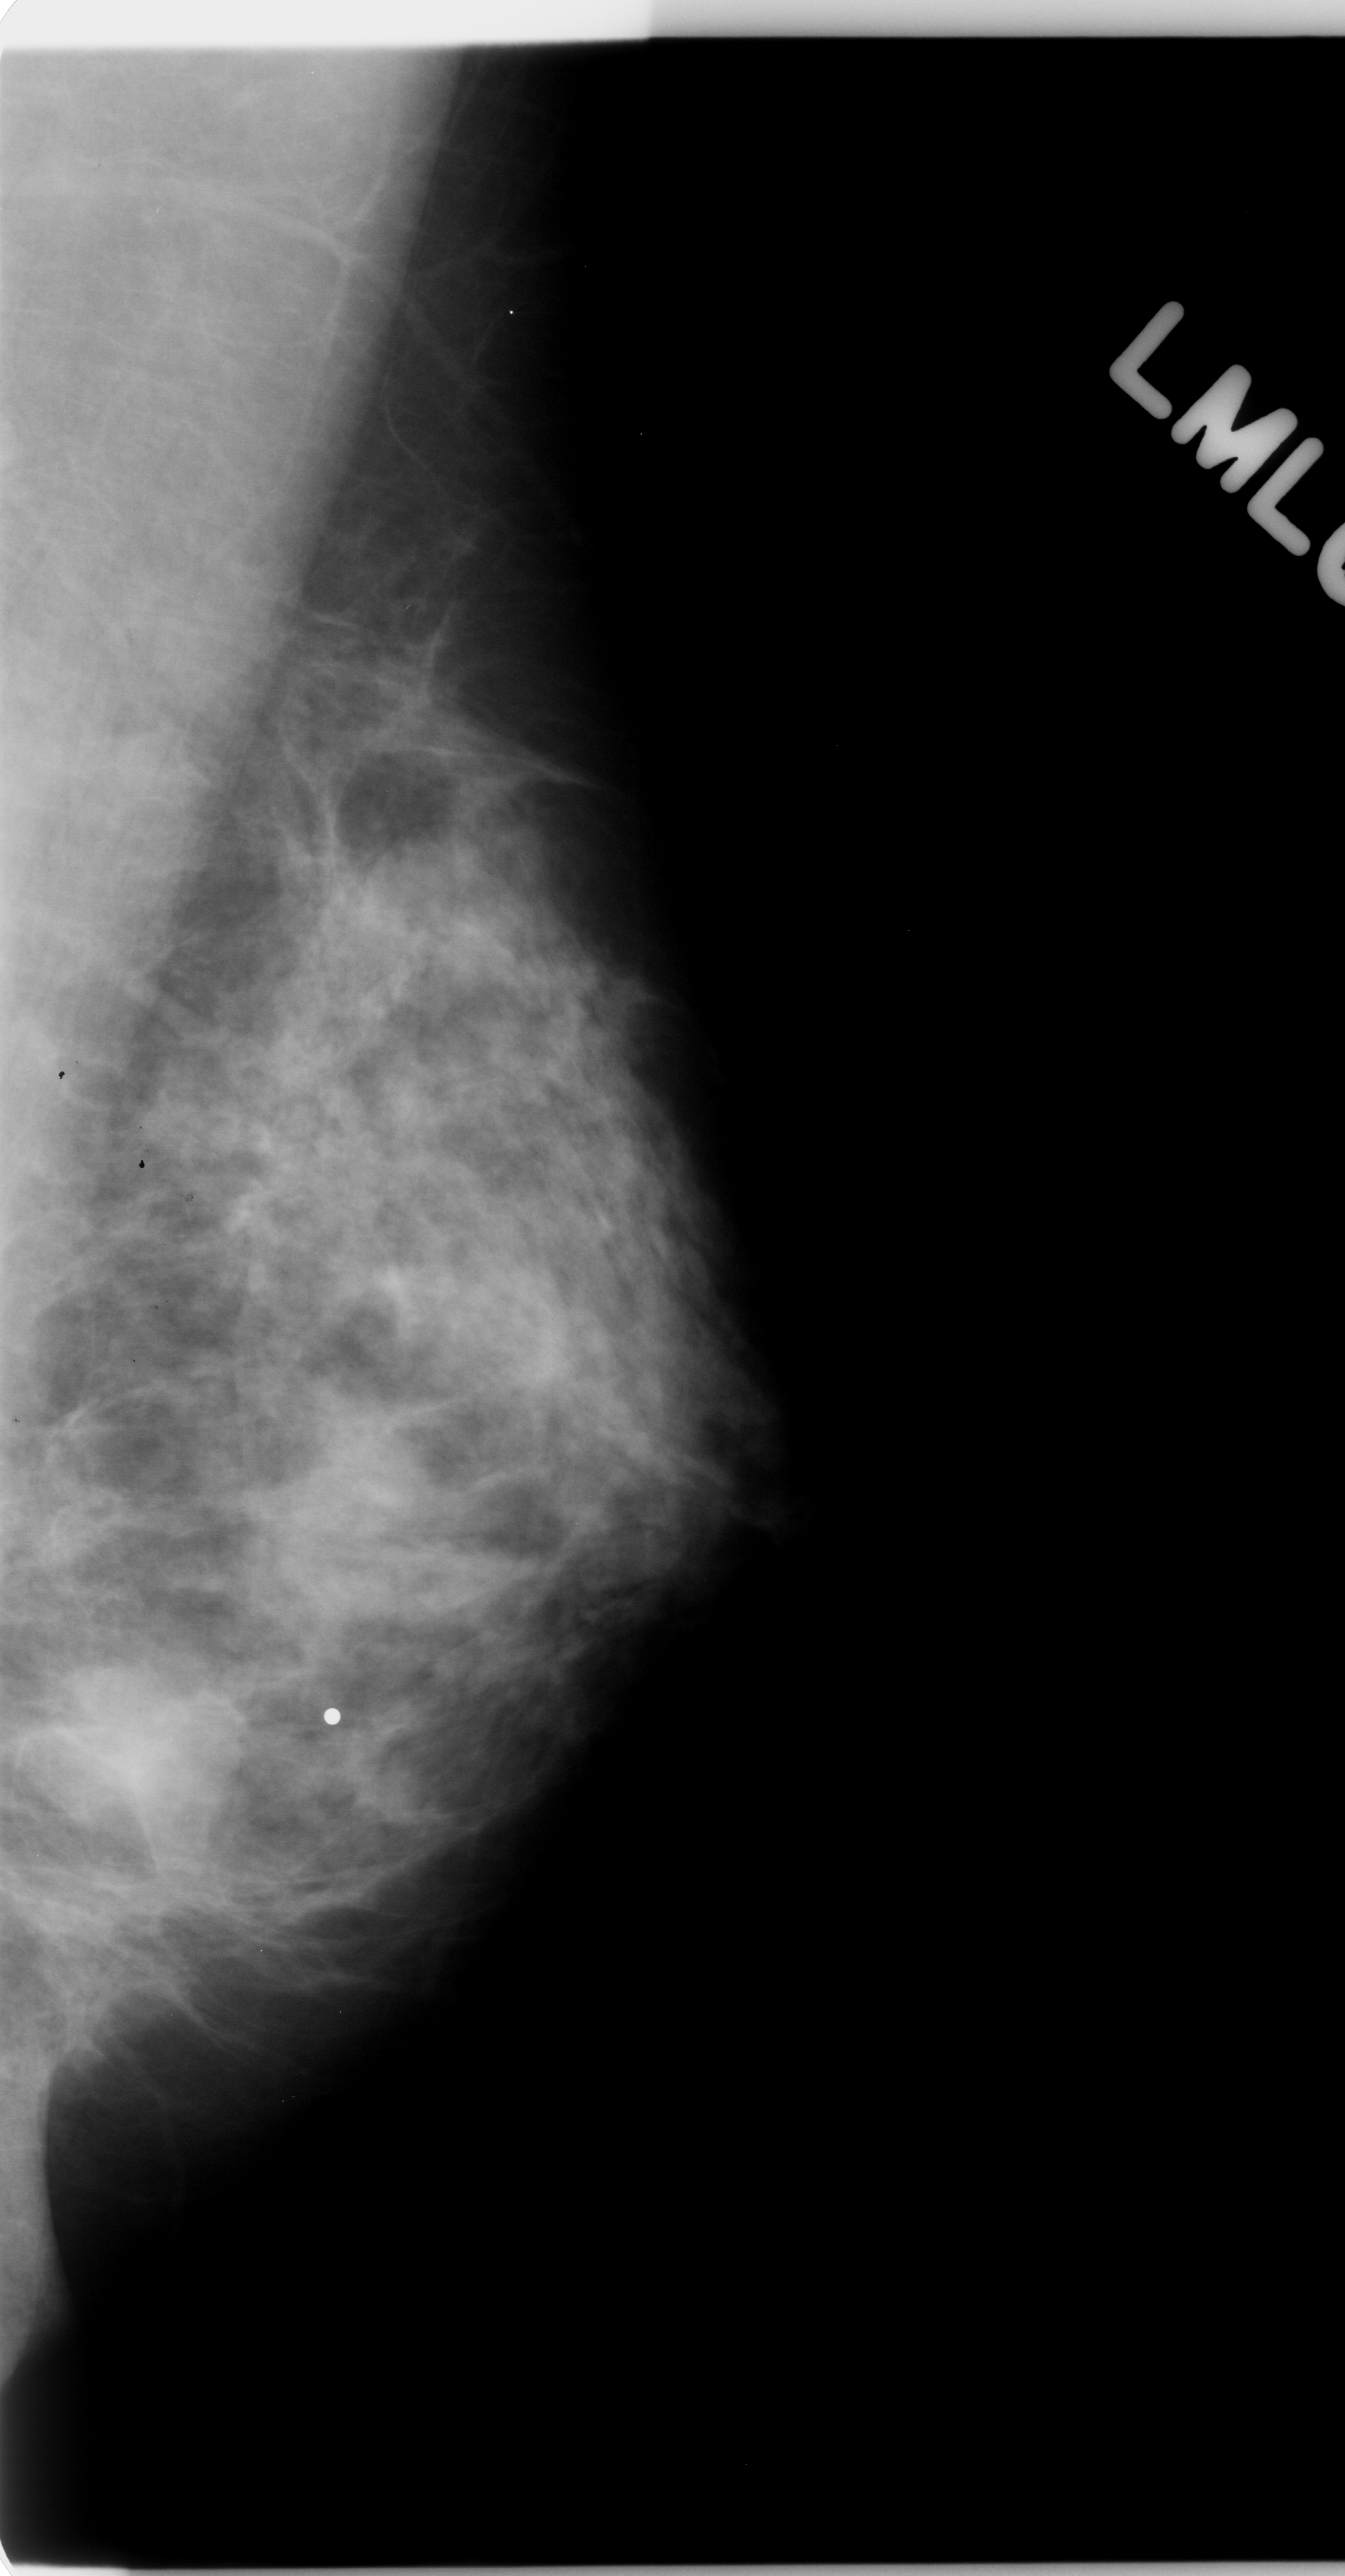
Mammogram (digitized film); left breast; MLO view; breast composition: scattered fibroglandular densities (BI-RADS density category 2 of 4); 1345 × 2576 image matrix.
Marked abnormalities (boxes around the expert regions of interest):
- mass, shape lobulated, margins ill defined; BI-RADS assessment category 4; subtlety rating 4 on a 1 (subtle) to 5 (obvious) scale; pathology (as recorded): malignant: box from (x=0, y=1628) to (x=251, y=1872) px